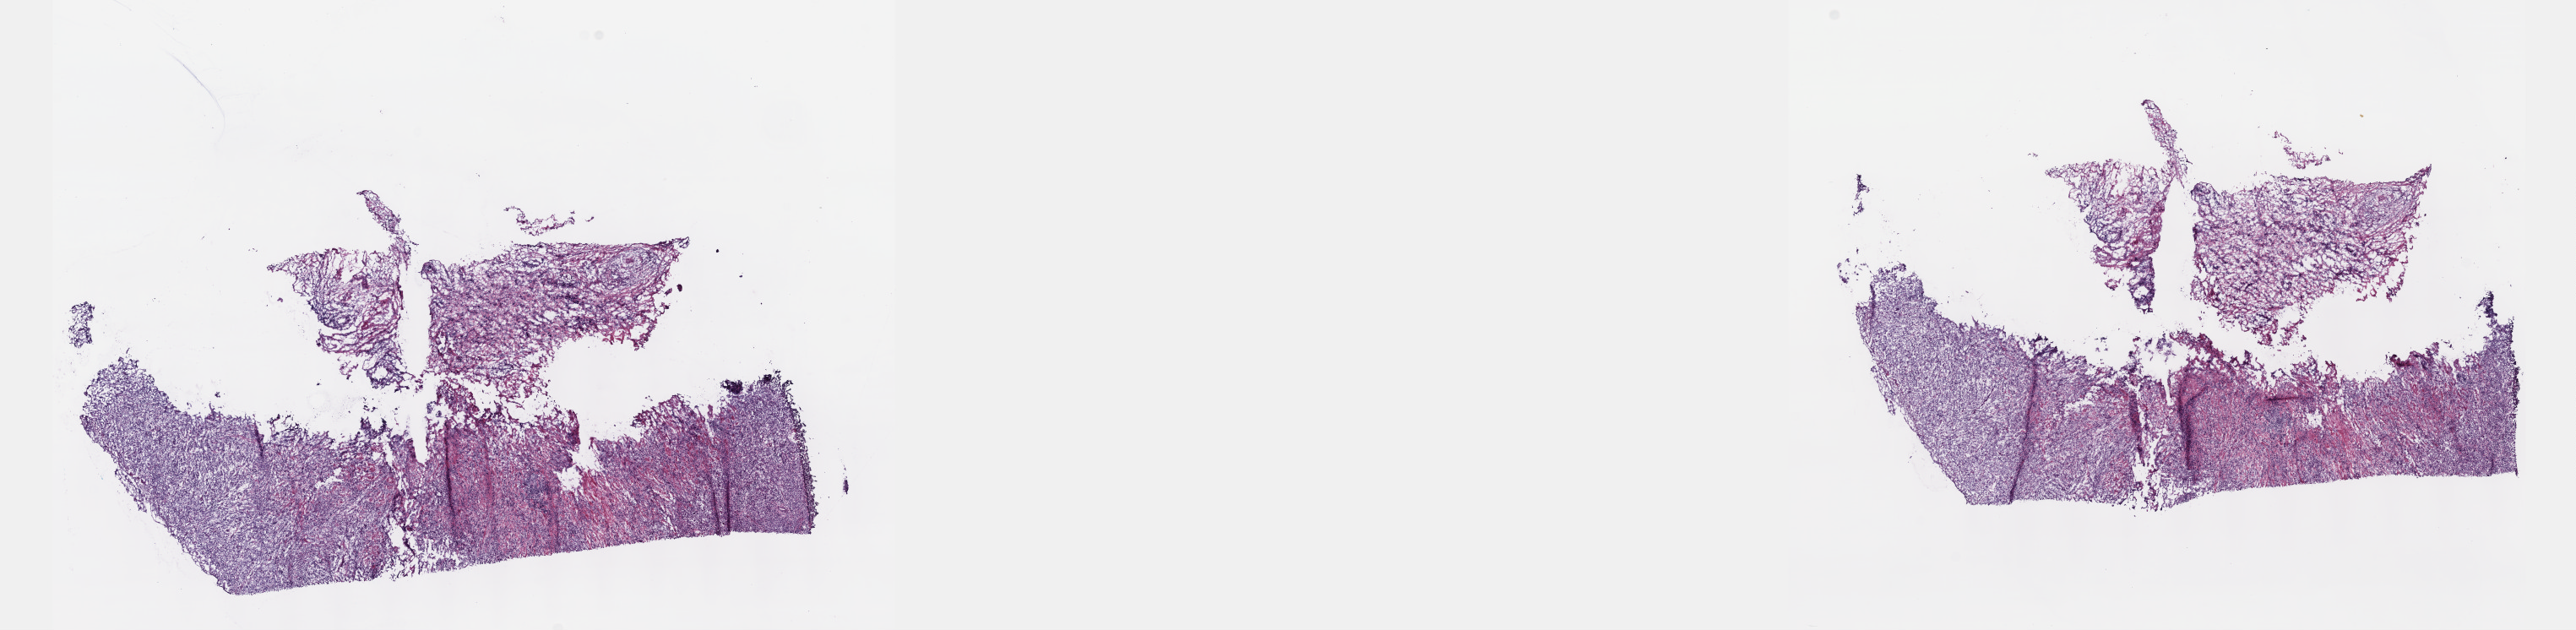
Whole-slide histology image, Hematoxylin and eosin (H&E) stained — whole scanned area (about 24.6 x 6.0 mm, from a 40x scan) shown as a low-resolution overview, frozen section from the top of the tissue portion, esophagus, primary tumour sample. Male patient. Histologic grade: G3 (poorly differentiated). Composition of this section per pathologist review: tumour cells 100%, tumour nuclei 65%, normal cells 0%, stromal cells 0%, necrosis 0%. Infiltration values recorded for this section: lymphocyte infiltration 5%, monocyte infiltration 0%, neutrophil infiltration 0%.
- diagnosis: Adenocarcinoma, NOS (lower third of esophagus)
- AJCC pathologic stage: IIA (5th edition)